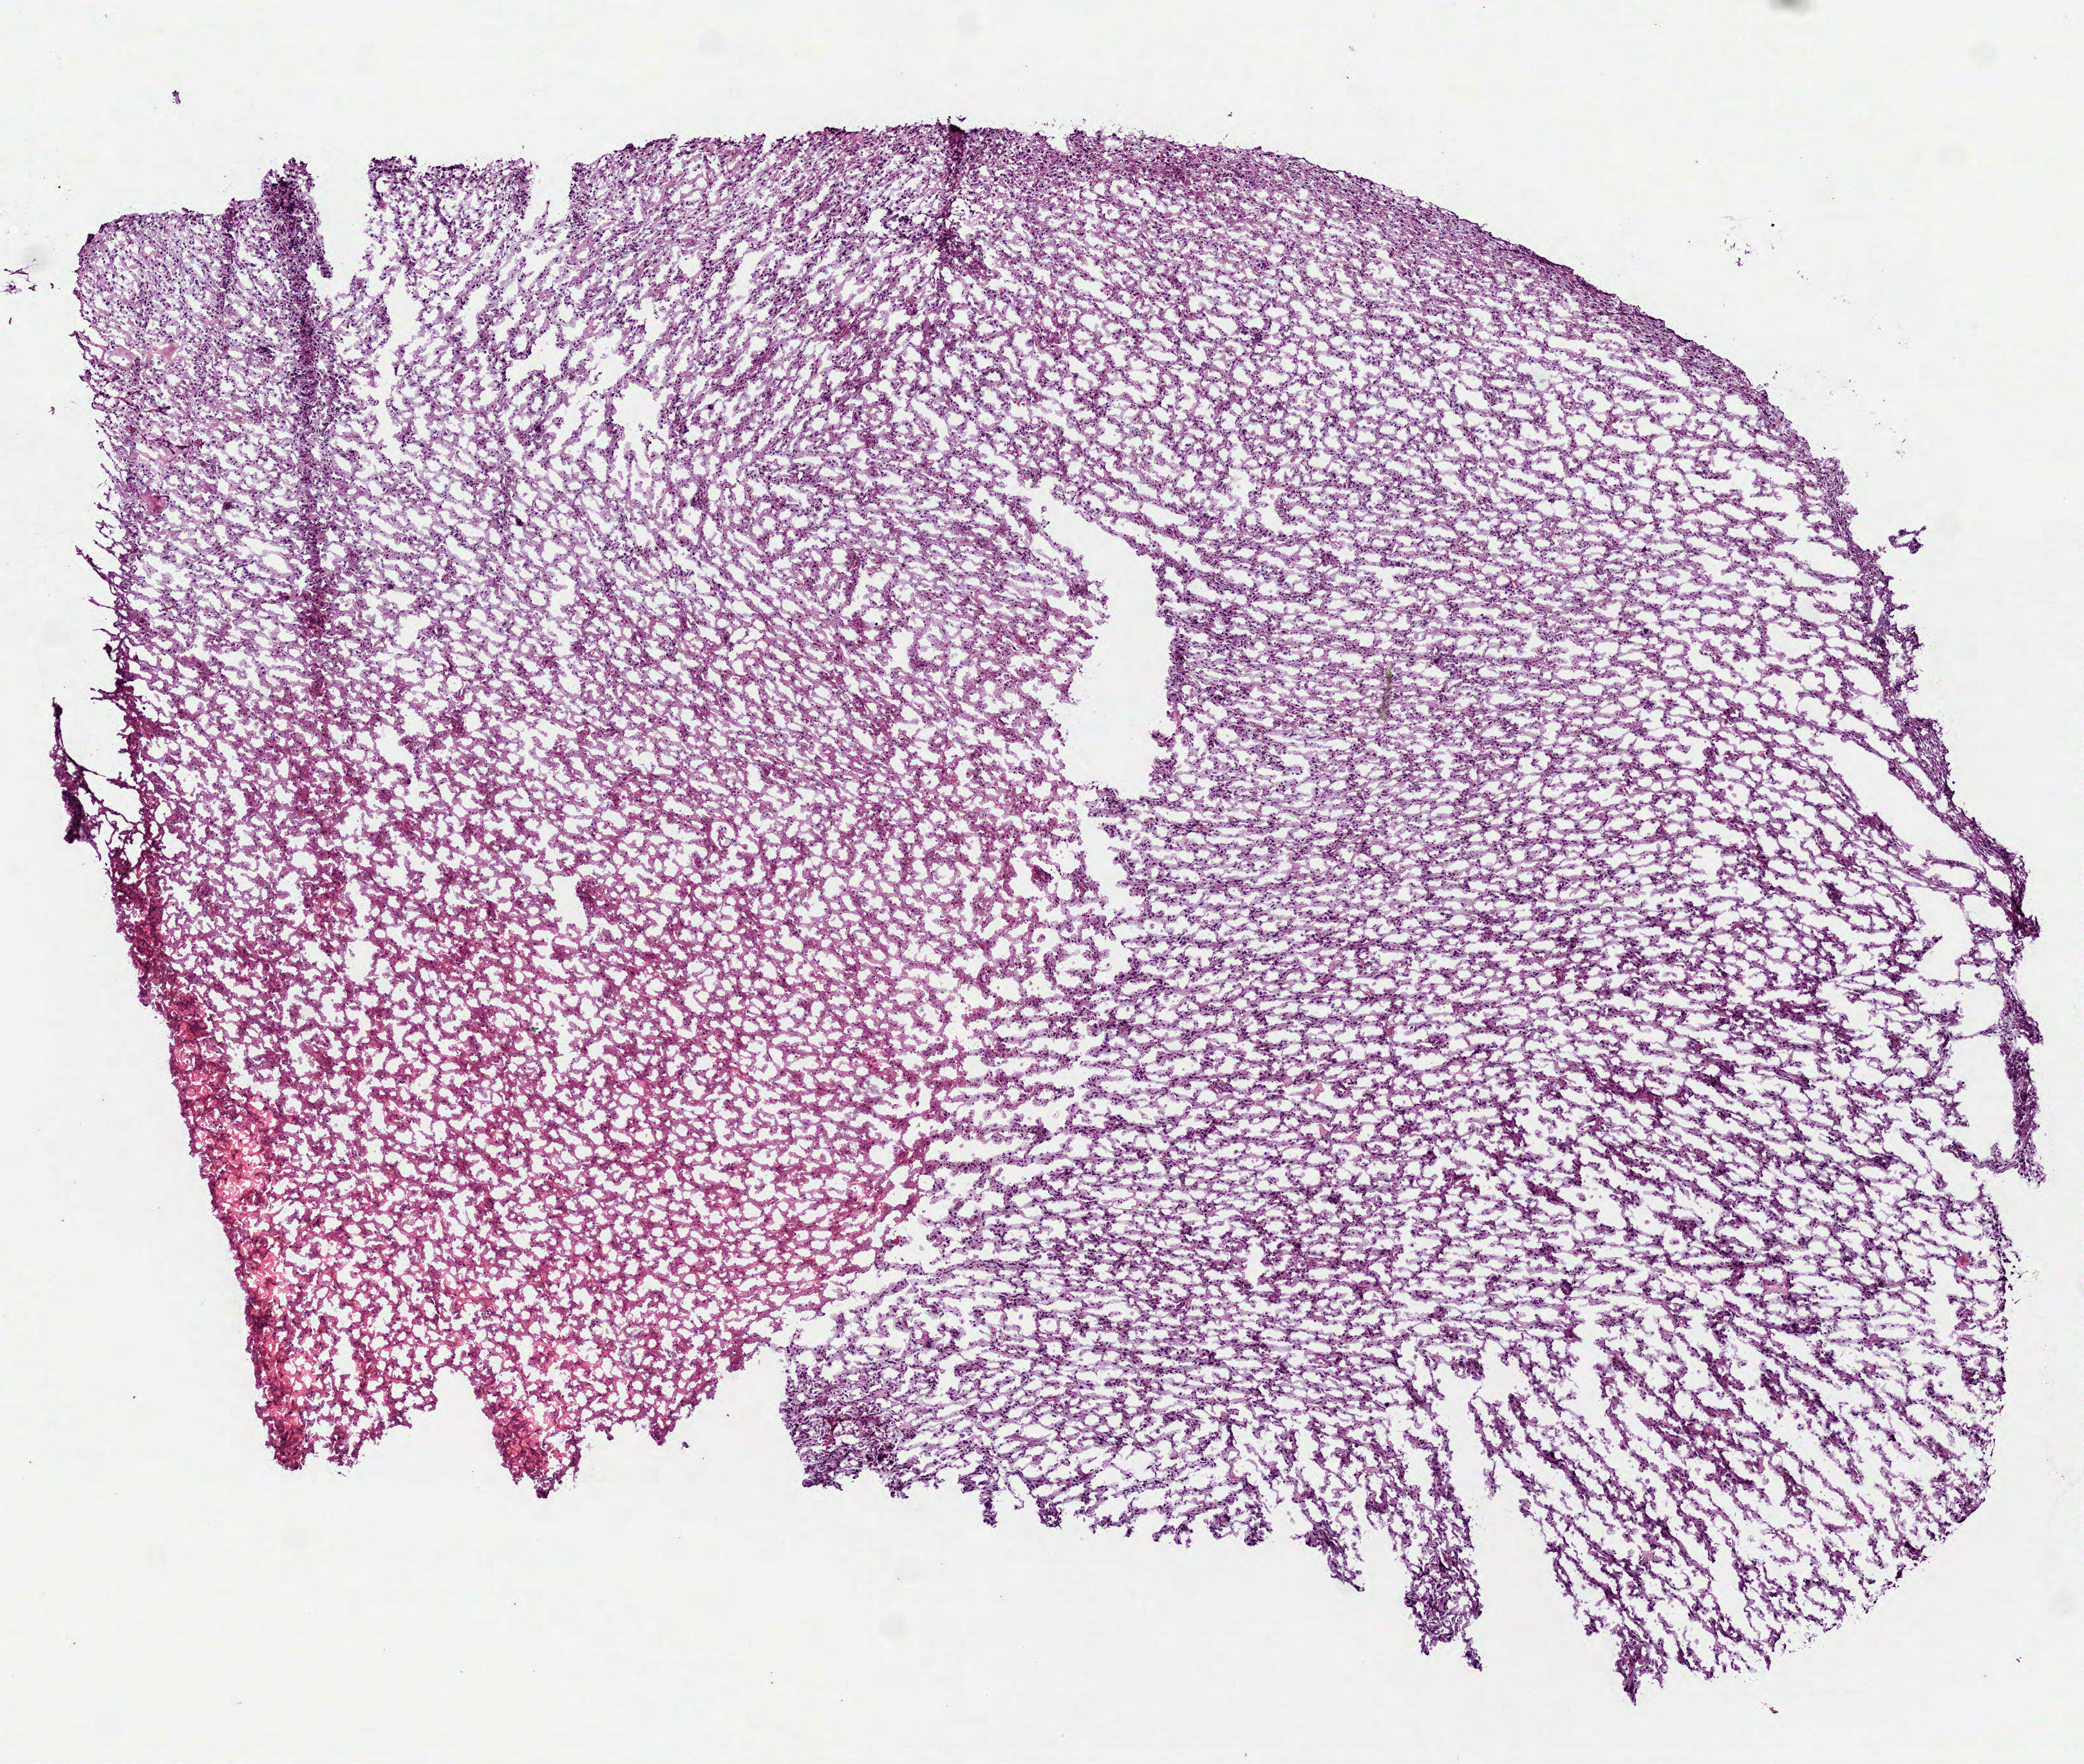
Digitized H&E tissue section (whole slide) — a low-resolution overview of the entire scanned area, about 6.5 x 5.5 mm. Frozen section from the bottom of the tissue portion. Sample: primary tumour, brain. Male, age 58 years at initial diagnosis. Histologic grade: G3 (poorly differentiated). Slide review estimates, as recorded: tumour cells 100%, tumour nuclei 75%, normal cells 0%, stromal cells 0%, necrosis 0%.
* laterality: right
* pathologic diagnosis: Mixed glioma